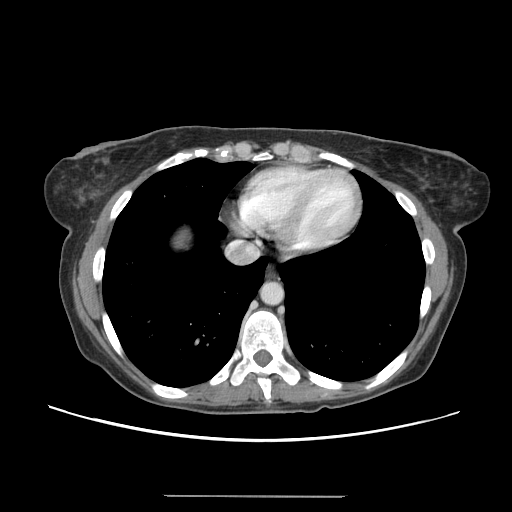
Contrast-enhanced abdominal CT, one axial slice. Slice 136 of 144 in the series (ordered by position). Intravenous contrast given. Soft-tissue window (W 400 / L 40 HU). 512 × 512 image matrix, field of view 380 × 380 mm. Female patient, age 53 years. From the clinical record (not read from this slice): diagnosis: colorectal cancer liver metastases, imaged before liver resection; multiple liver metastases: yes; largest metastasis: 1.1 cm.
Outlined on this slice (manually delineated by an expert):
- liver: box from (x=171, y=226) to (x=193, y=254) px
- planned liver remnant (the part of the liver to remain after resection): (x=169, y=226)–(x=193, y=254)